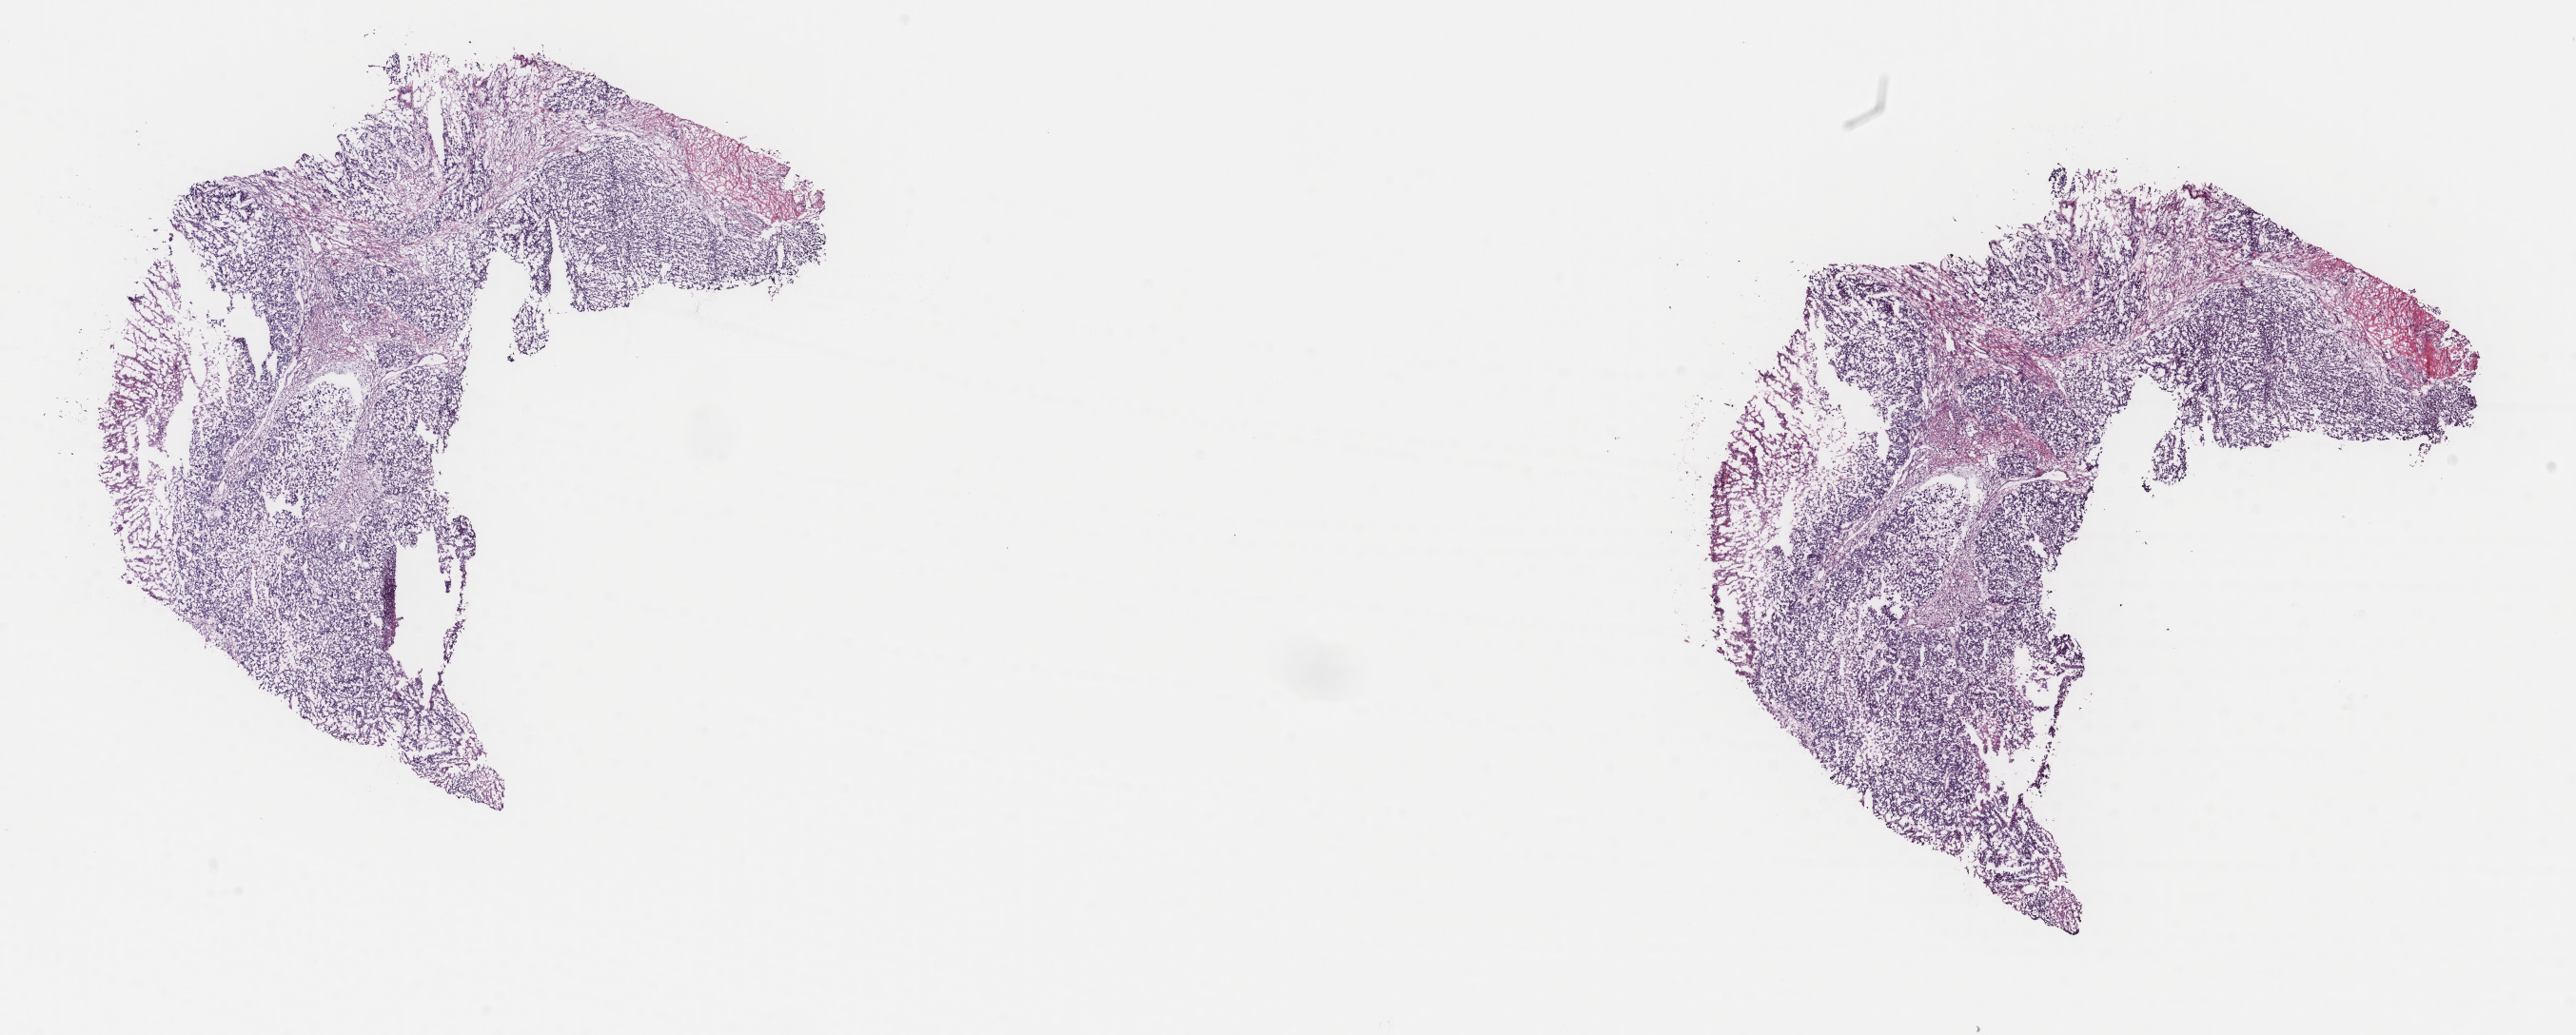
Whole-slide histology image, Hematoxylin and eosin (H&E) stained, shown as a low-resolution overview of the whole scanned area (about 21.5 x 8.6 mm); frozen section from the top of the tissue portion; metastatic tumour sample. Male patient; age at initial diagnosis 69 years. Slide review estimates, as recorded: tumour cells 85%, tumour nuclei 85%, normal cells 0%, stromal cells 0%, necrosis 15%. Infiltration values recorded for this section: lymphocyte infiltration 0%, monocyte infiltration 0%, neutrophil infiltration 0%.
* this section: metastatic tumour tissue
* patient diagnosis: Malignant melanoma, NOS